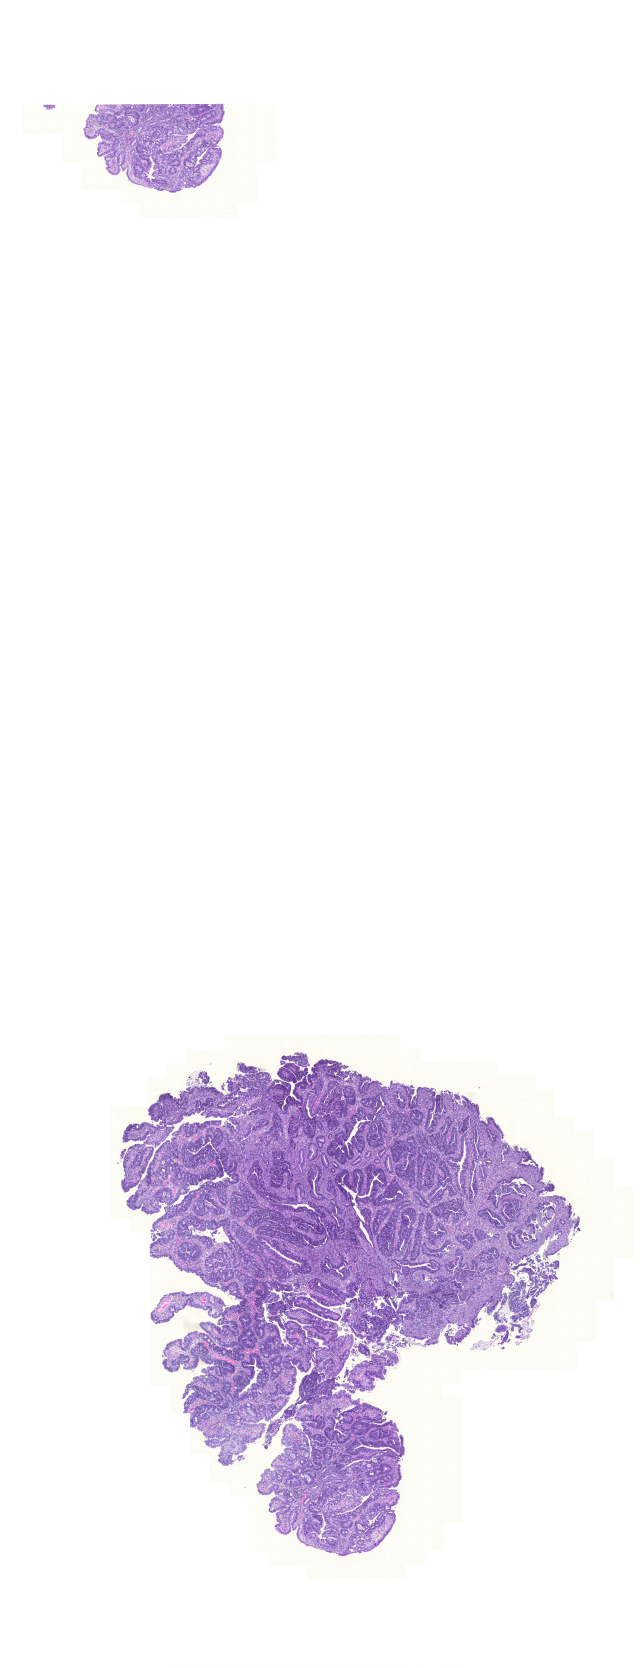
Whole-slide histology image, Hematoxylin and eosin (H&E) stained, whole scanned area (about 9.6 x 24.8 mm) shown as a low-resolution overview, FFPE section, primary tumour sample from the rectum. Patient: female, age at initial diagnosis 68 years.
Histologic diagnosis: Adenocarcinoma, NOS. AJCC pathologic stage: IV (6th edition).